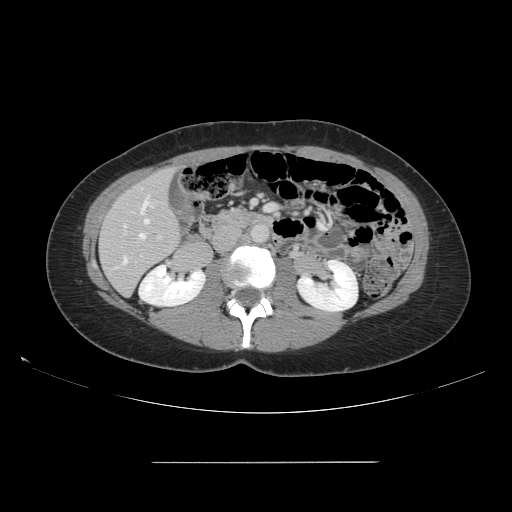
Contrast-enhanced abdominal CT, one axial slice; 120 kVp; soft-tissue window (W 400 / L 40 HU); 512 × 512 image matrix, field of view 421 × 421 mm. Female patient, age 46 years. From the clinical record (not read from this slice): diagnosis: colorectal cancer liver metastases, imaged before liver resection; multiple liver metastases: yes.
Annotated regions visible in this slice (expert manual segmentation):
- hepatic veins: bounding box [x1, y1, x2, y2] px = [123, 198, 152, 265]
- liver: [100, 169, 180, 295]
- planned liver remnant (the part of the liver to remain after resection): [99, 169, 180, 295]
- portal vein (with intrahepatic branches): [158, 236, 161, 239]